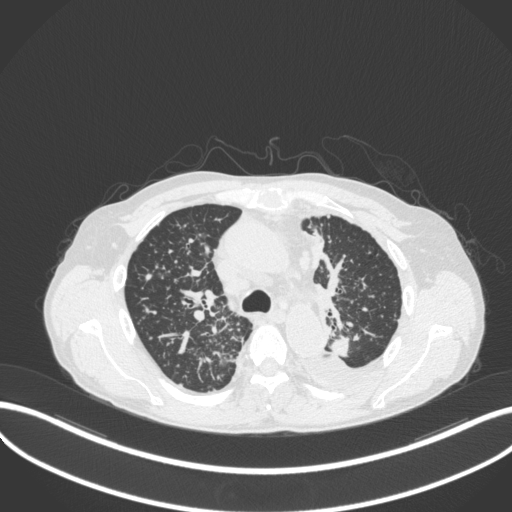
Chest CT, one axial slice; position 250 of 319 along the scan axis; 120 kVp; lung window (W 1500 / L -600 HU); 1 mm slice thickness; 512 × 512 image matrix, field of view 400 × 400 mm. Patient: male, 58 years. Case-level facts recorded for this patient, not image findings: clinical TNM (as recorded): T1c N3 M1.
Structures marked on this image (rectangle marked by the reading radiologist):
- lung tumour (recorded histology: adenocarcinoma): bounding box (x1, y1, x2, y2) in pixels: (326, 333, 357, 361)